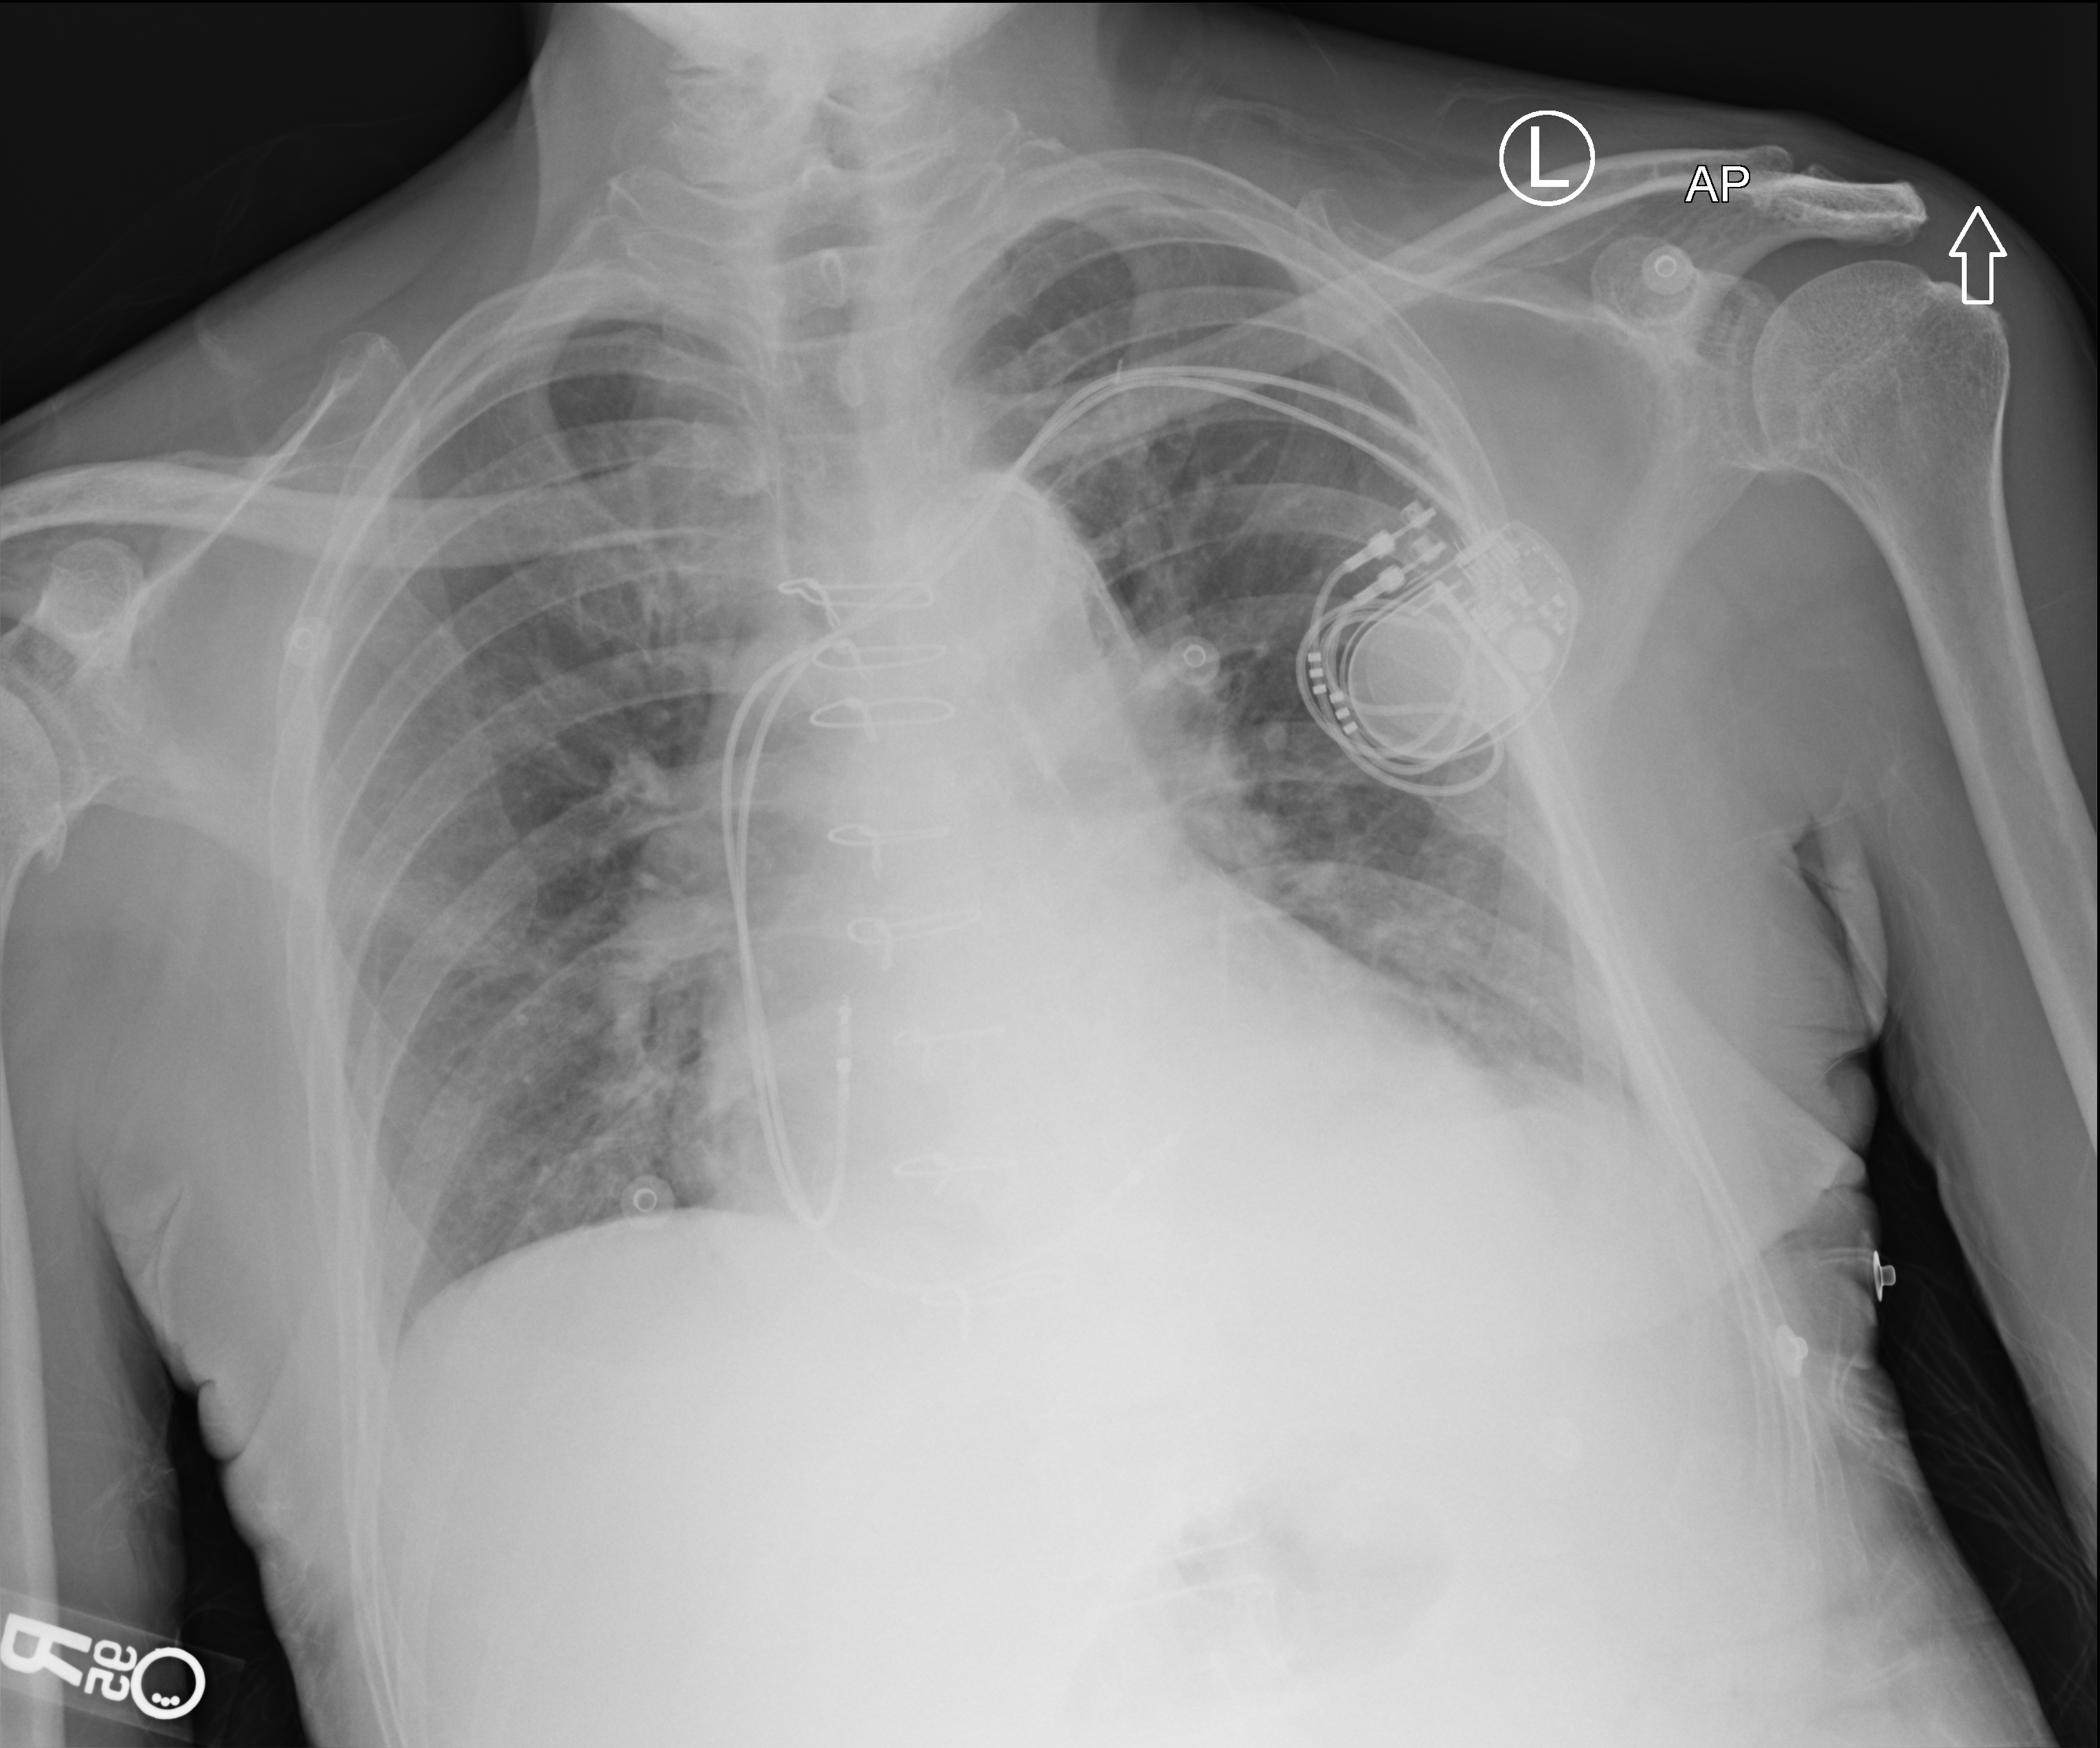
Chest radiograph, anteroposterior (AP) projection. Male patient hospitalised with COVID-19, age 60–74 years.
Hospital-stay facts (about this admission, not read from this image; timing relative to this image not recorded):
- admitted to intensive care during this hospital stay: no